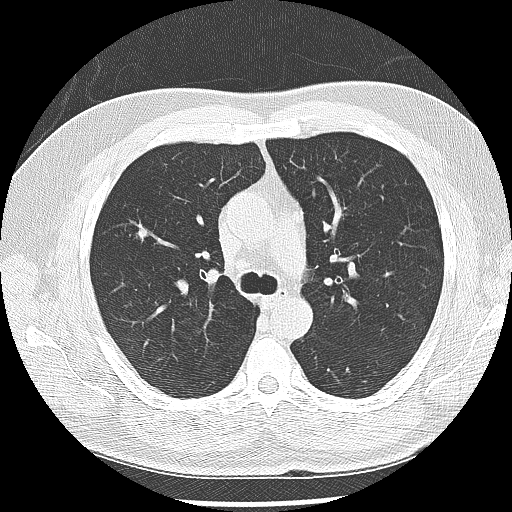
Low-dose screening chest CT, one axial slice. Position 178 of 265 along the scan axis. 120 kVp. Lung window (W 1500 / L -600 HU). 512 × 512 image matrix, field of view 340 × 340 mm.
Outlined on this slice (manually delineated by an expert):
- lesion 1 (tumor, upper lobe of right lung): bounding box (x1, y1, x2, y2) in pixels: (137, 222, 152, 243)